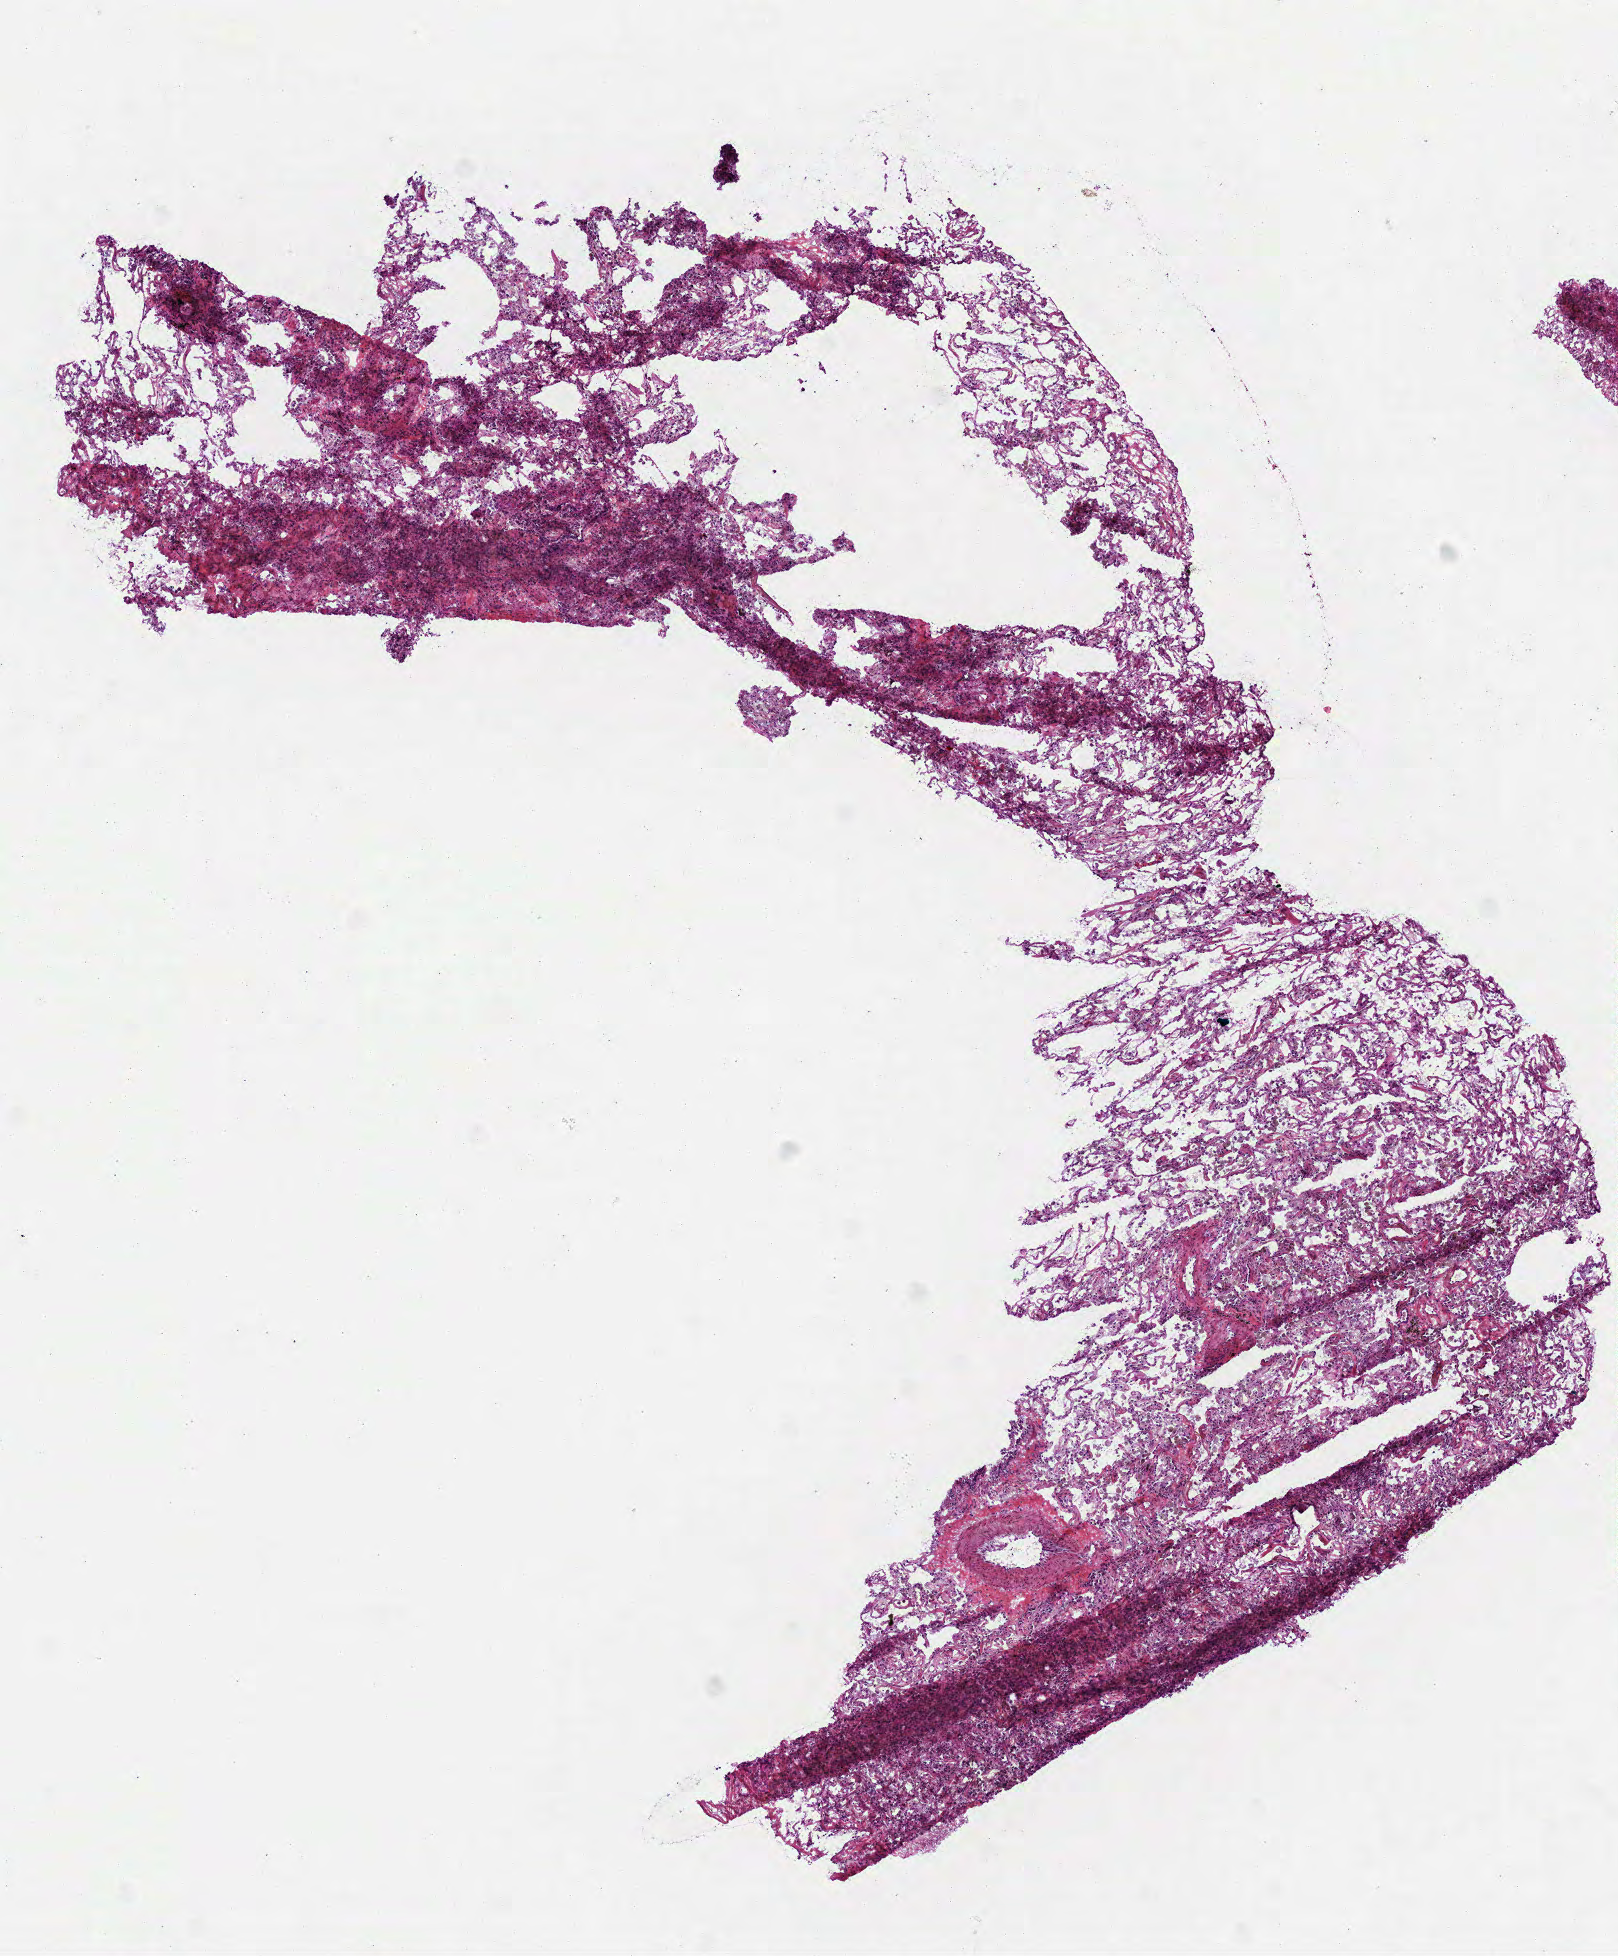
Hematoxylin and eosin (H&E) stained whole-slide image — low-resolution overview of the scanned area, about 6.5 x 7.9 mm. Frozen section. Solid tissue normal (non-tumour tissue) sample from the lung. Female, age 70 years at initial diagnosis.
This section: solid tissue normal sample (biorepository sample class). Patient diagnosis: Adenocarcinoma, NOS.